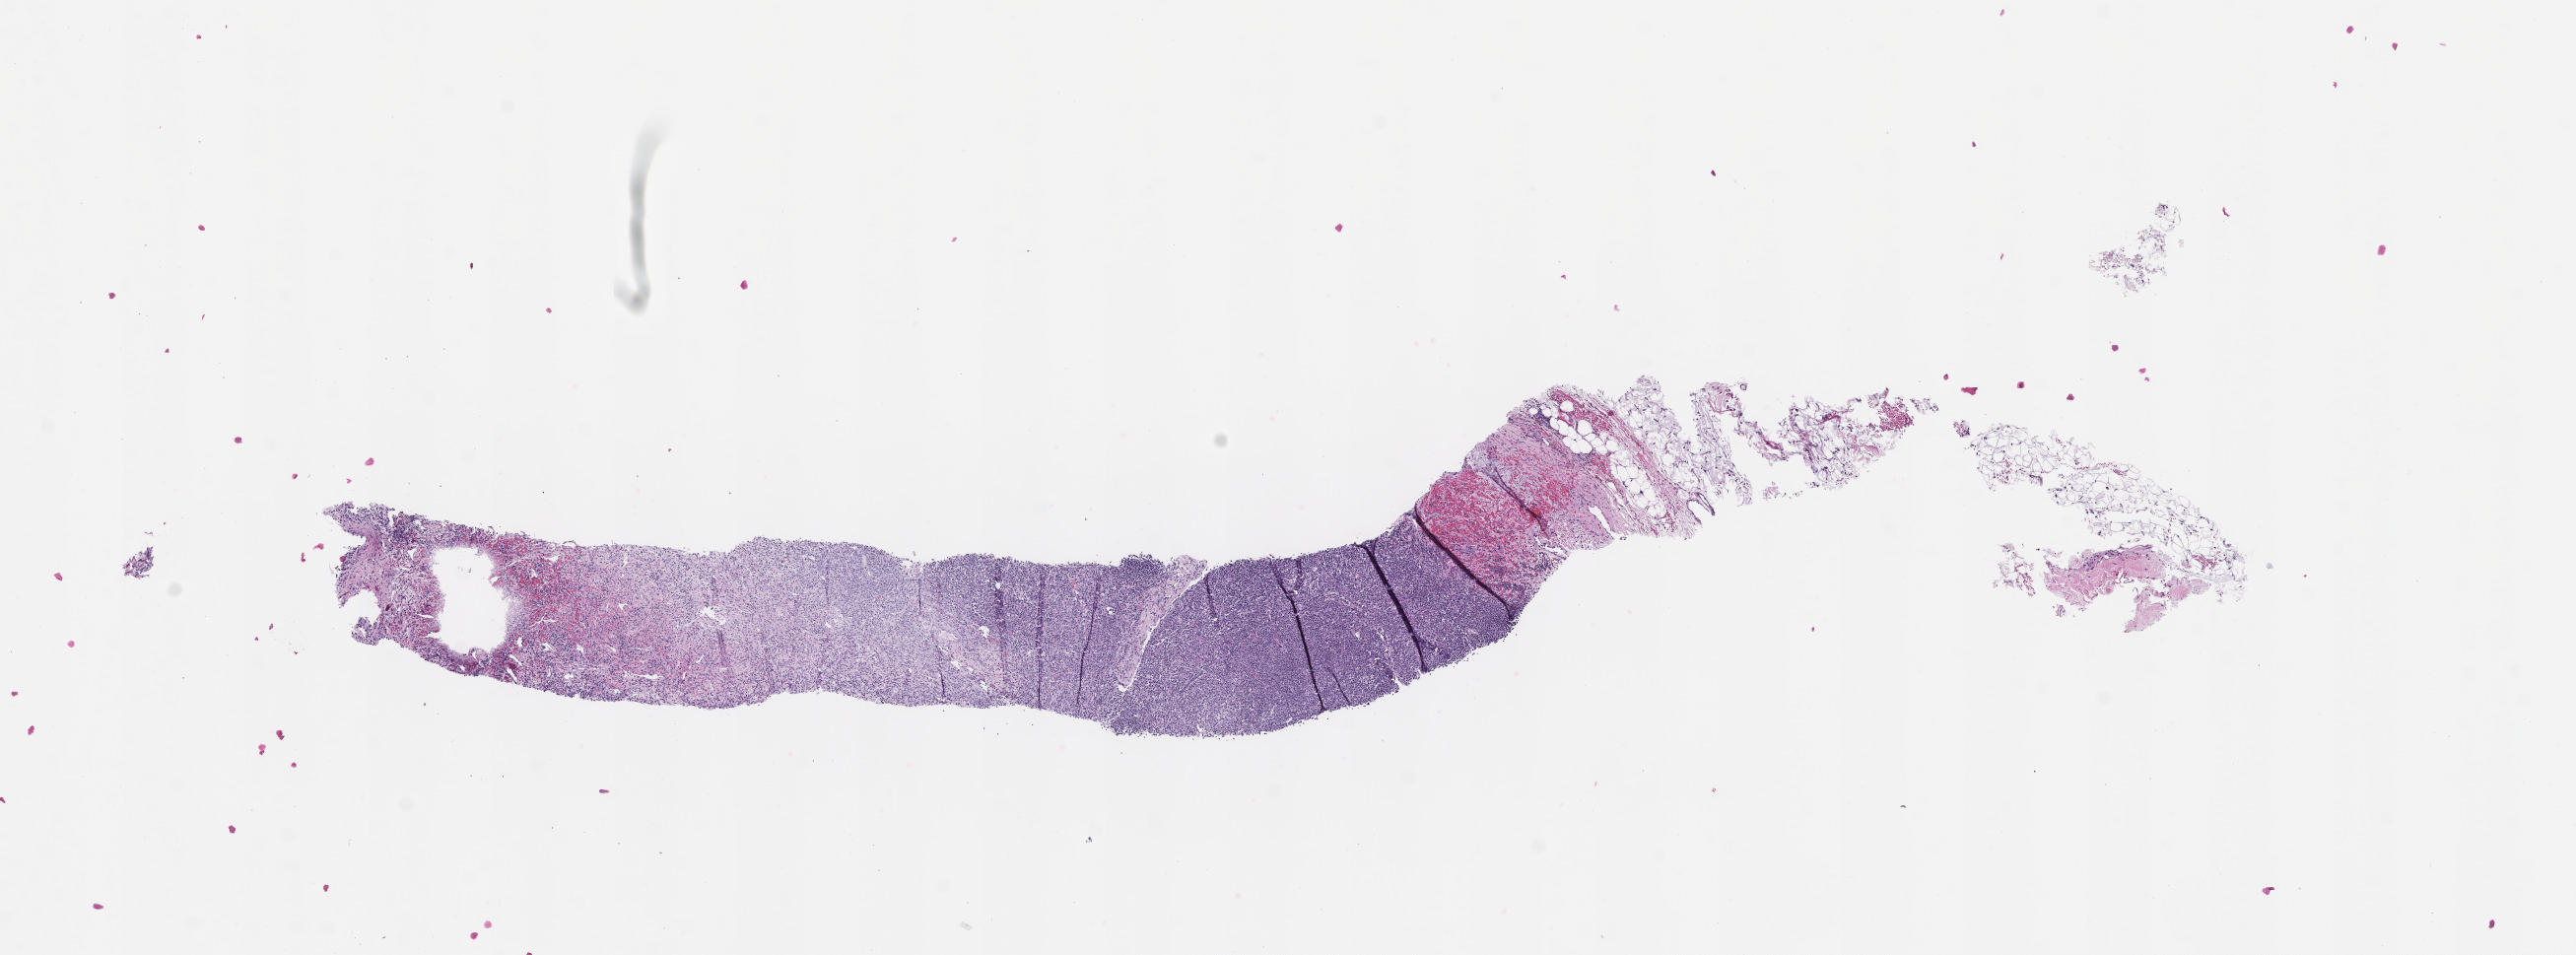
Whole-slide image, hematoxylin and eosin (H&E) stain, shown as a low-resolution overview of the whole scanned area (about 10.6 x 3.9 mm). Formalin-fixed, paraffin-embedded (FFPE) tissue. Patient: female.
This section: metastasis (sampled organ not recorded). Primary diagnosis of the patient: Ovarian Carcinoma.